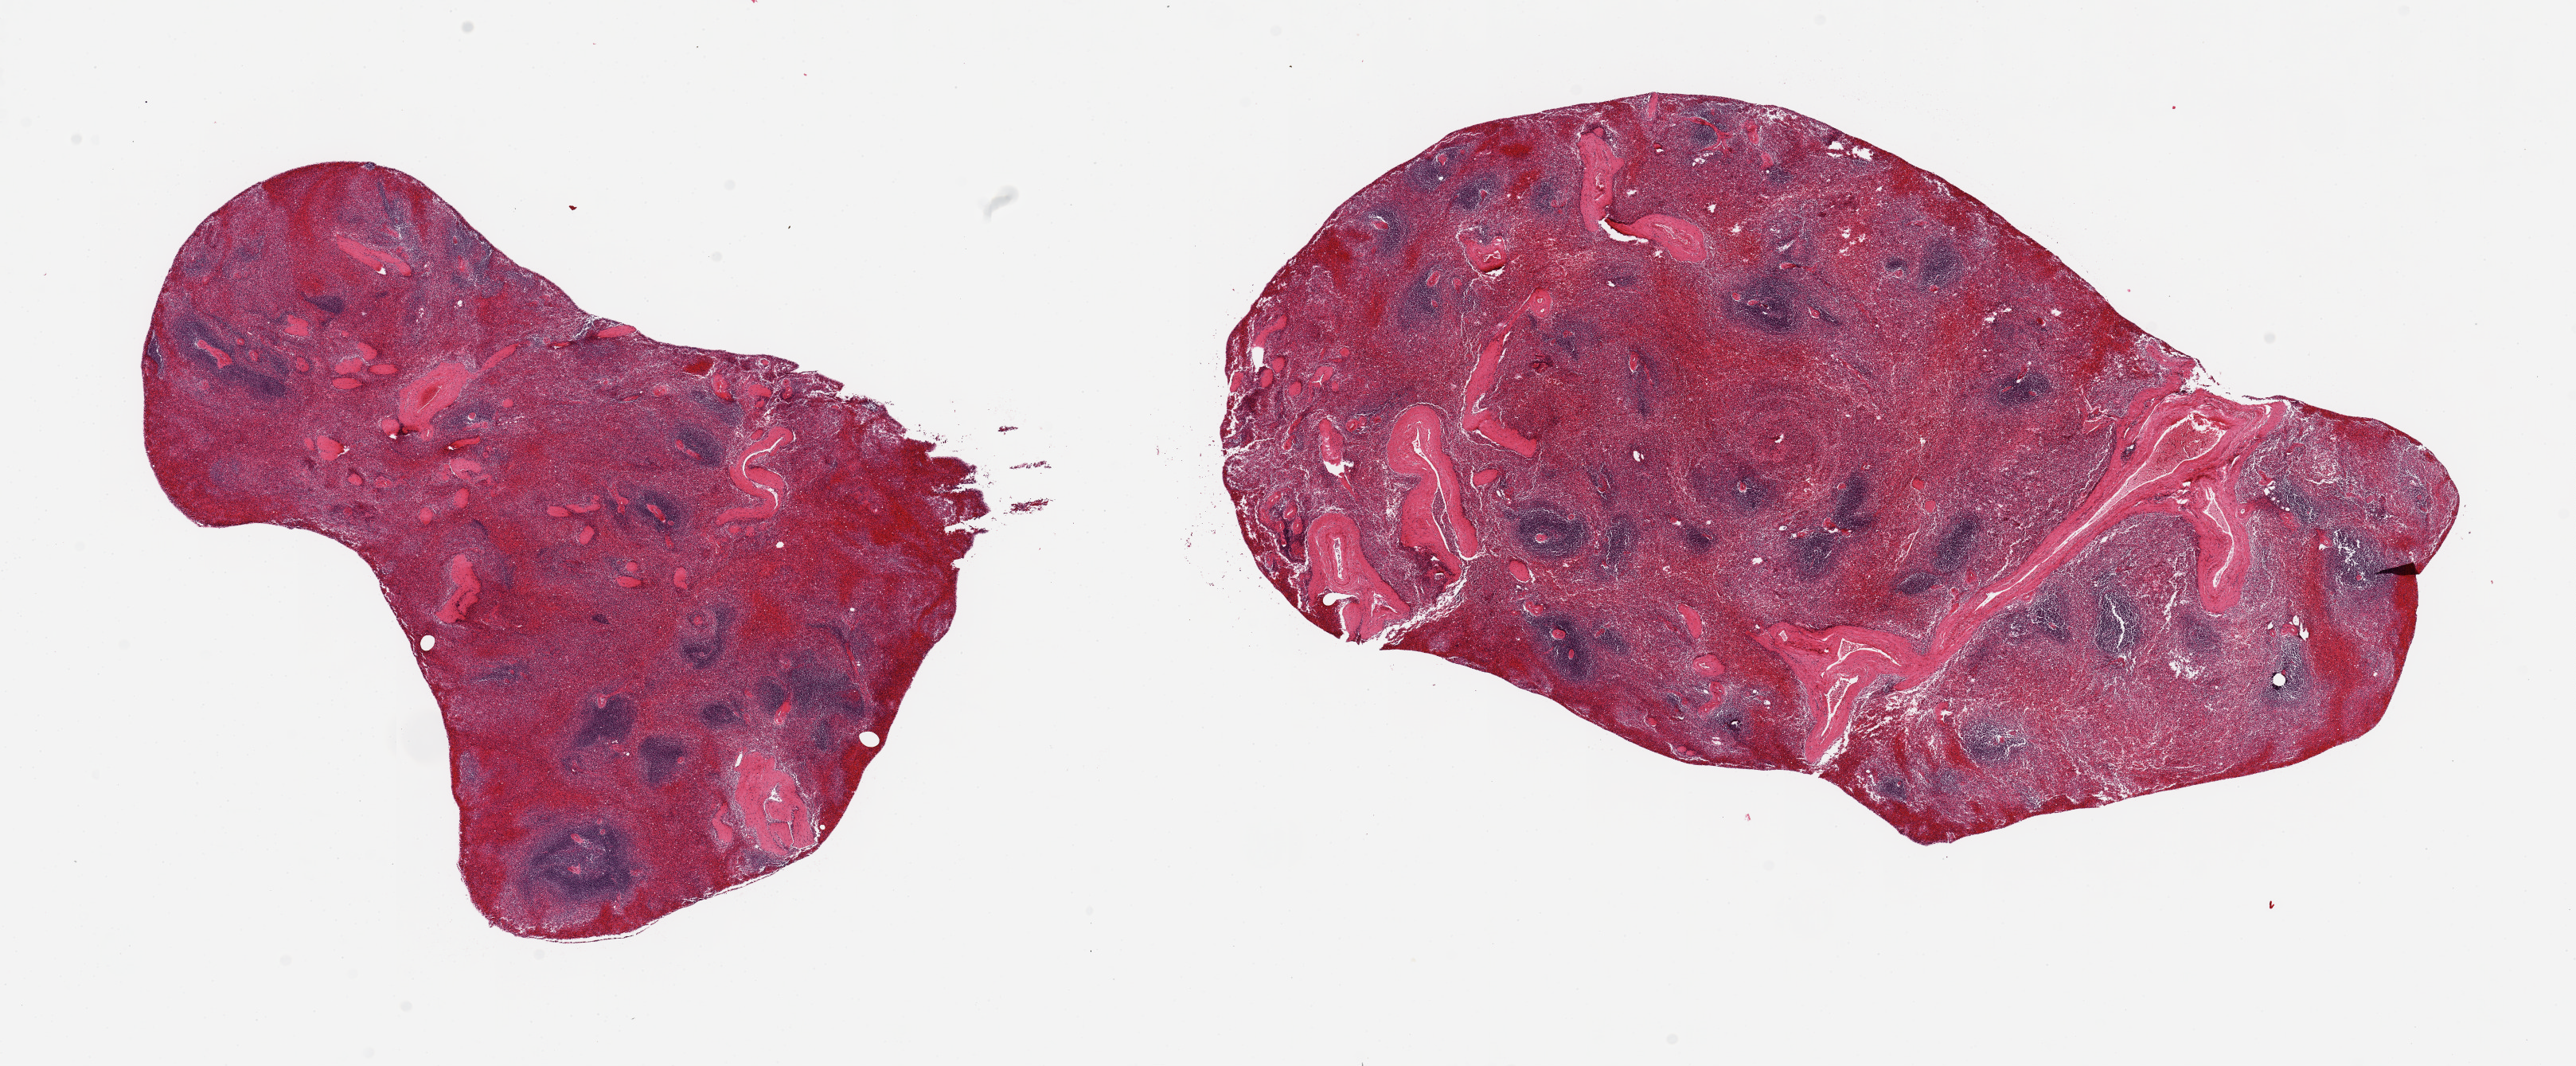
Whole-slide image, hematoxylin and eosin (H&E) stain, a low-resolution overview of the entire scanned area, about 25.6 x 10.6 mm (acquisition: 20x scan); PAXgene-fixed paraffin-embedded (PFPE) section; target tissue: spleen; donor tissue sample.
Review note (as recorded): 2 pieces; congested.